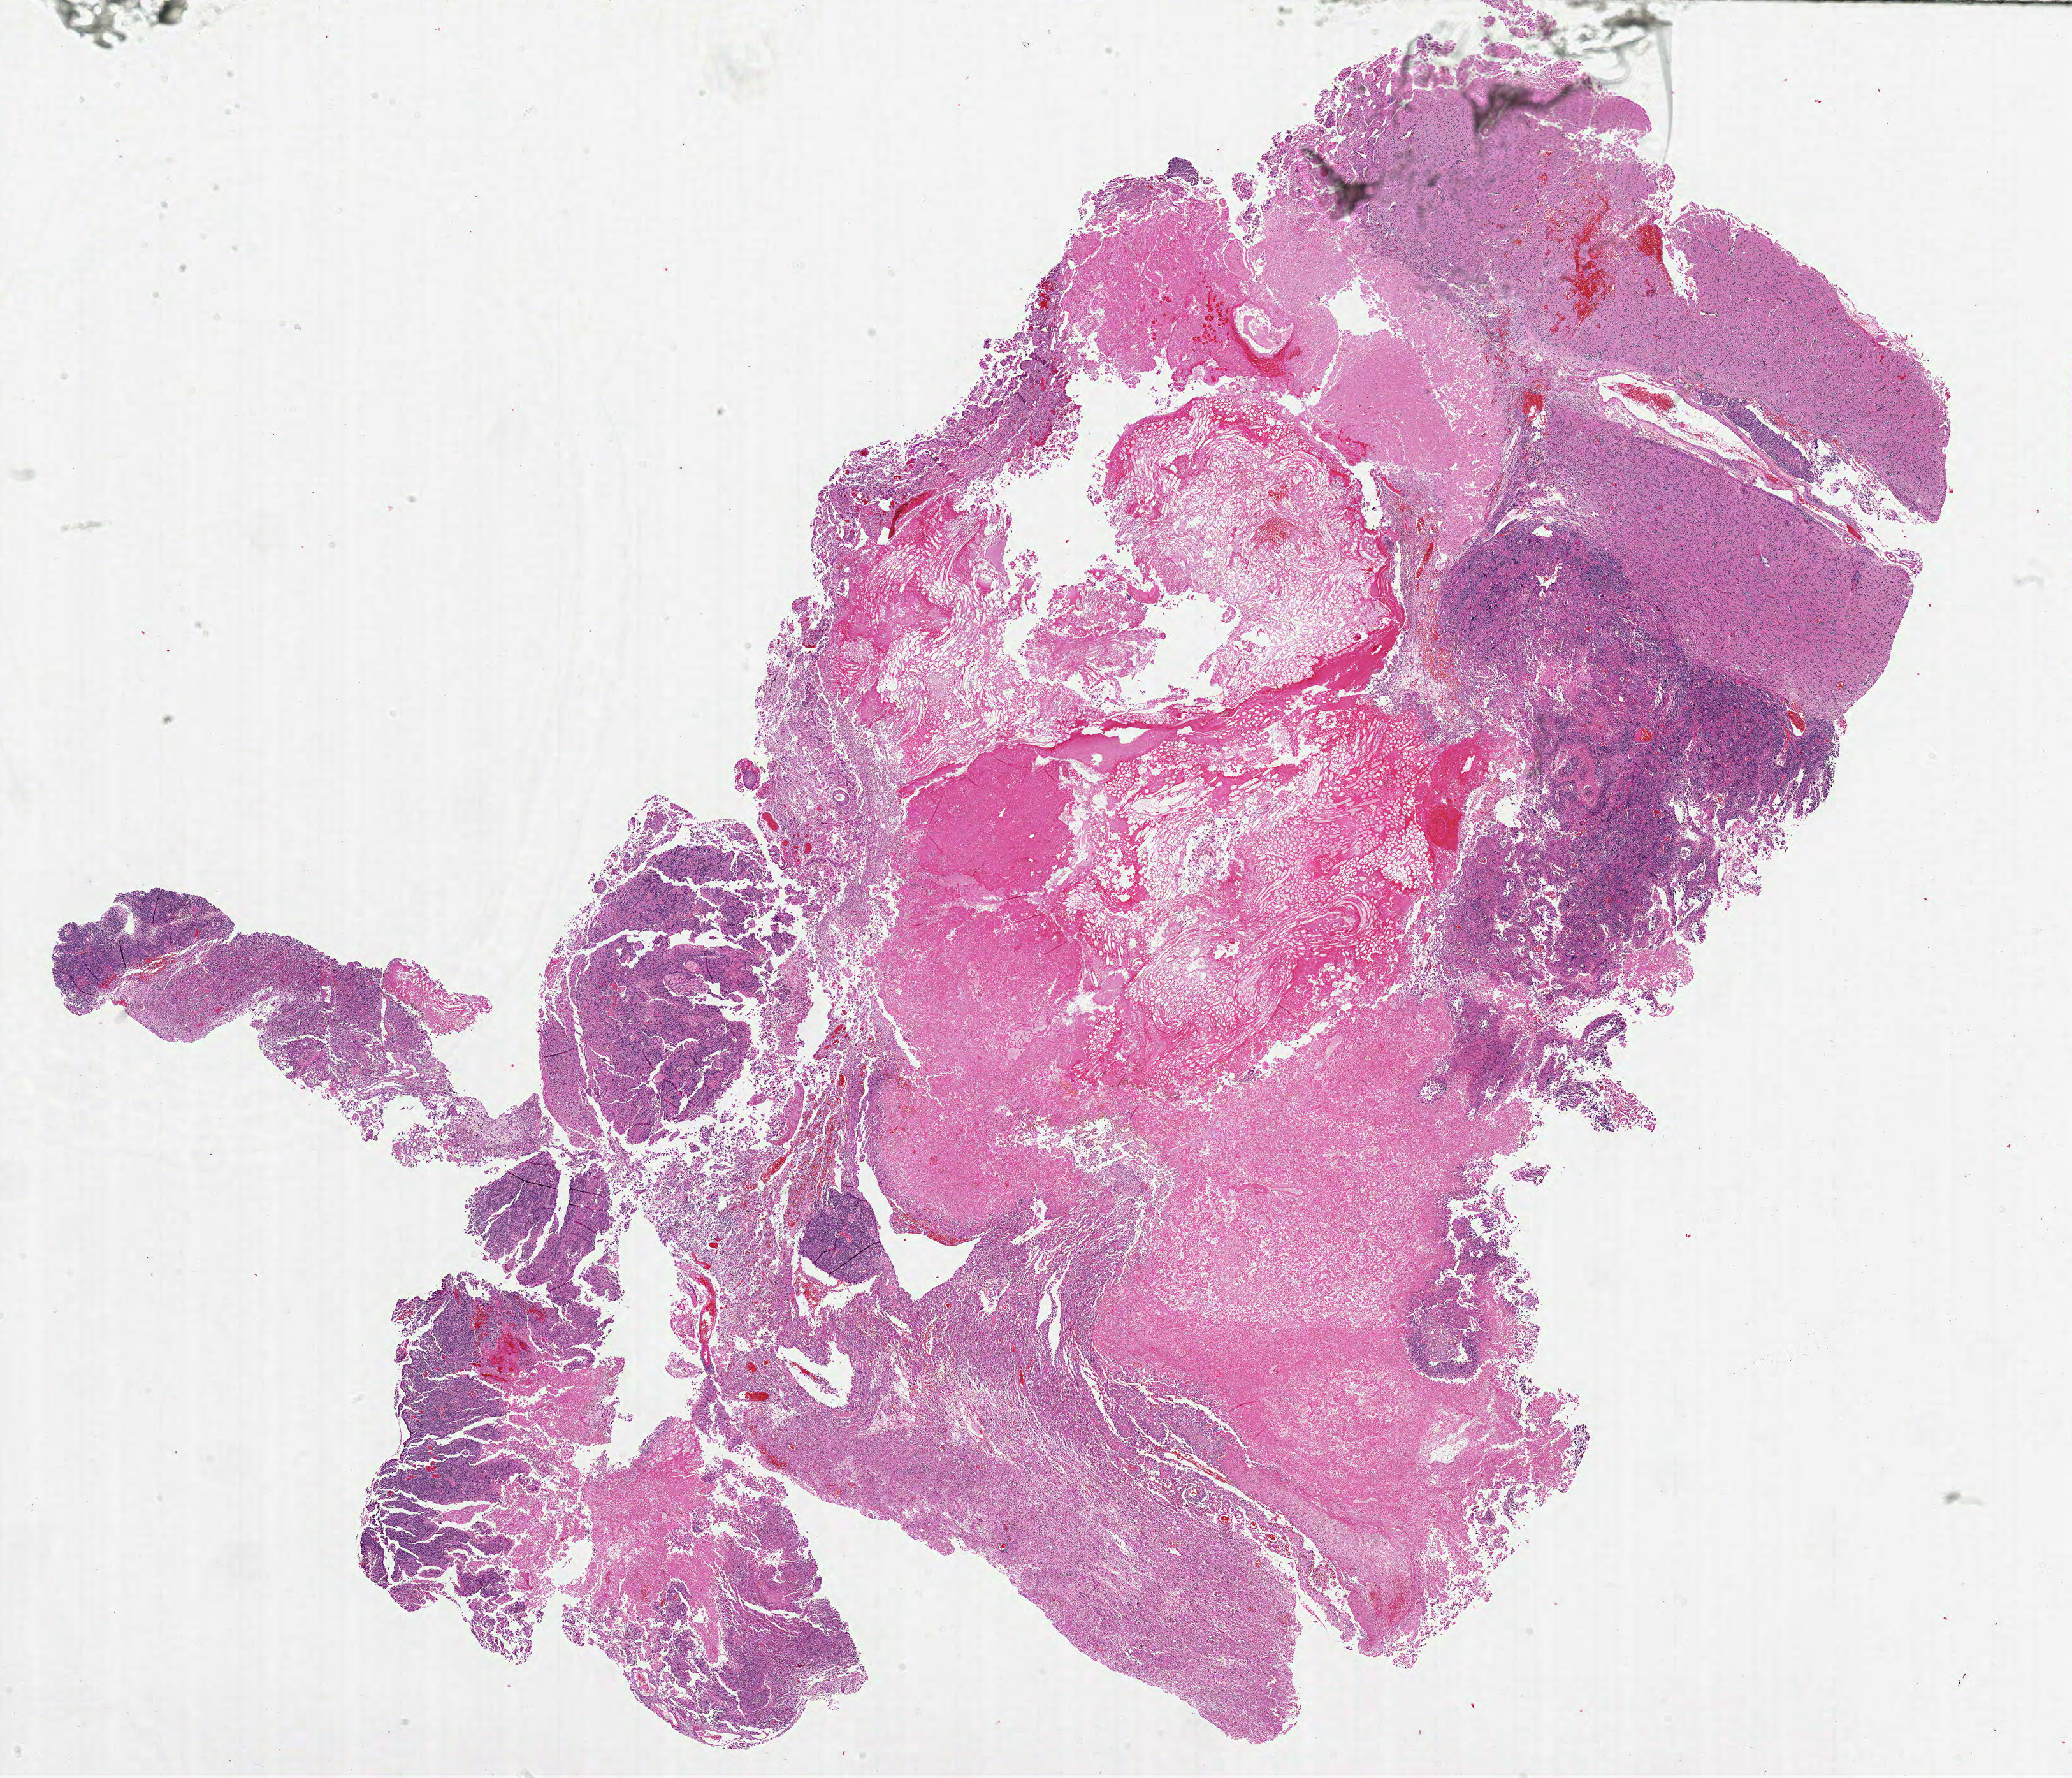
H&E-stained whole-slide image, low-resolution overview of the scanned area, about 26.0 x 22.3 mm (from a 20x scan). Formalin-fixed paraffin-embedded (FFPE) diagnostic section. Sample: primary tumour, brain. Male, age 24 years at initial diagnosis.
Histologic diagnosis: Glioblastoma.